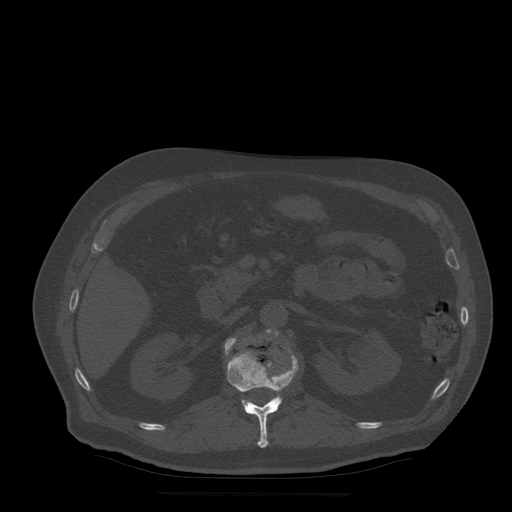
CT including the spine, one axial slice. Position 190 of 522 along the scan axis. Bone window (W 1800 / L 400 HU). 1.25 mm slice thickness. 512 × 512 image matrix. Patient age 72 years. Case-level facts recorded for this patient, not image findings: primary cancer: prostate.
Structures marked on this image (semi-automatically segmented with operator editing):
- L1 vertebra: box from (x=225, y=338) to (x=299, y=448) px
- L2 vertebra: (x=267, y=329)–(x=278, y=414)